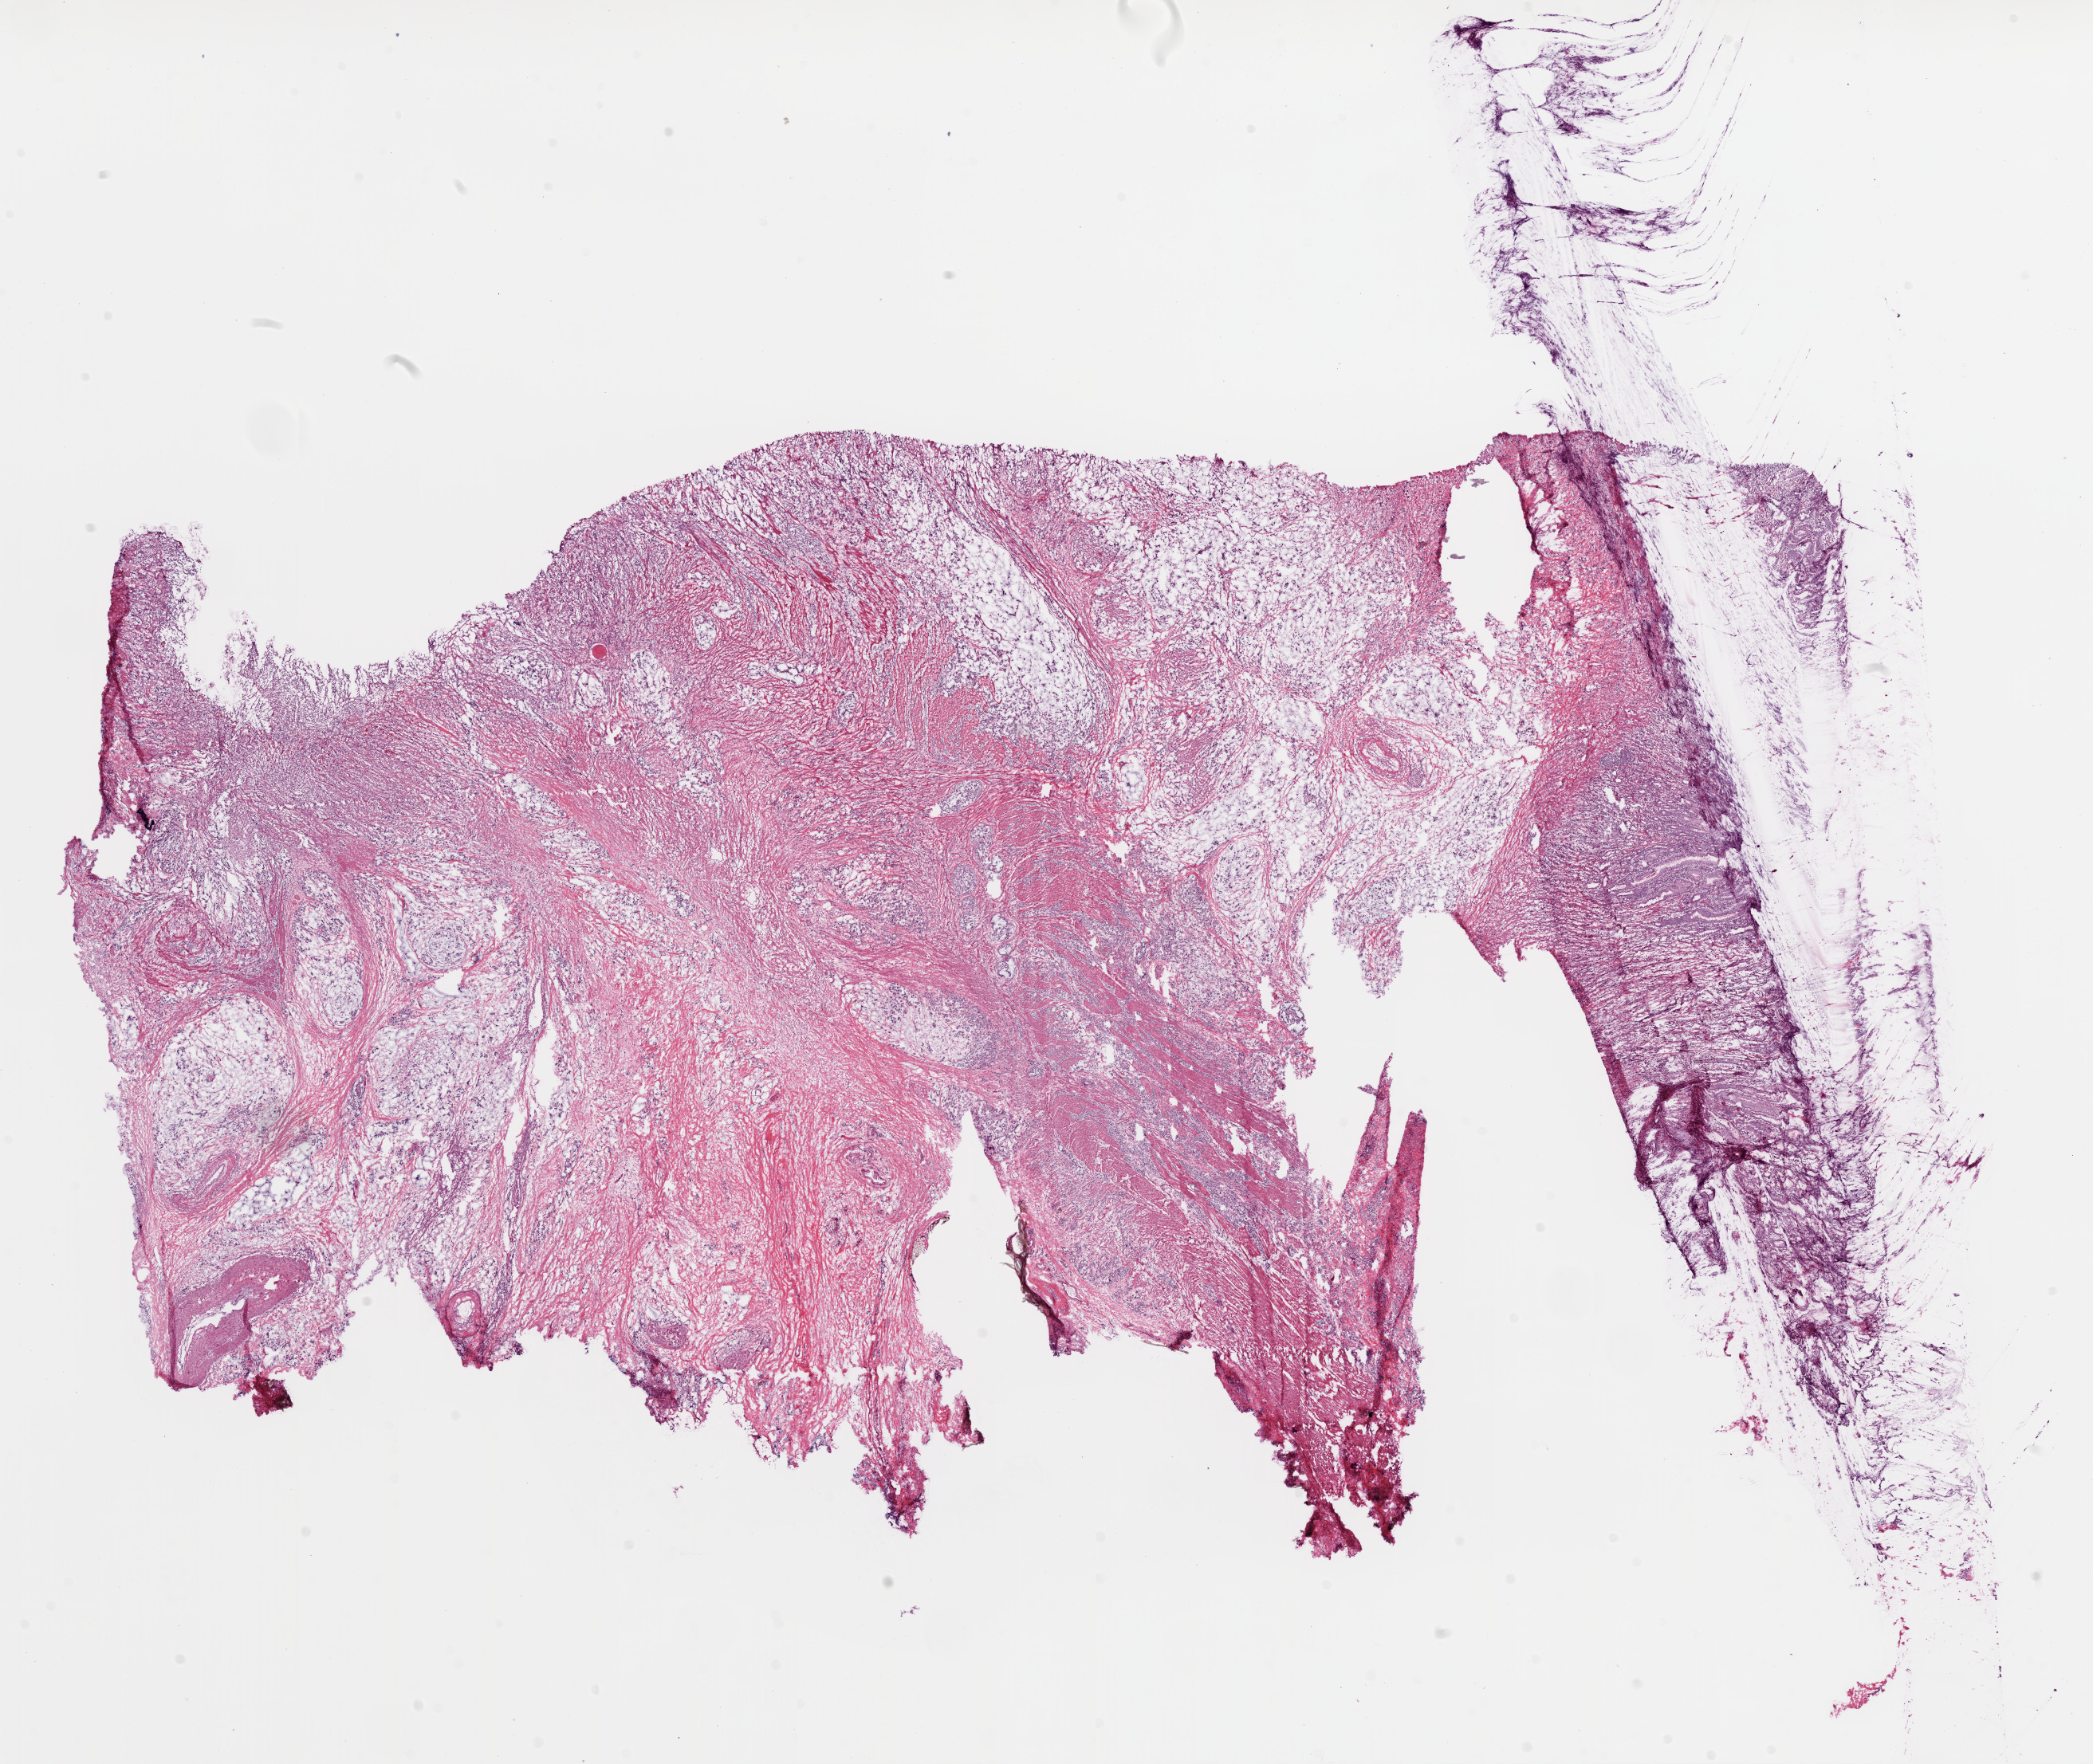
Whole-slide histology image, H&E-stained, shown as a low-resolution overview of the whole scanned area (about 21.1 x 17.8 mm, acquisition: 20x scan). Frozen section from the top of the tissue portion. Stomach, primary tumour sample. Male patient; age at initial diagnosis 43 years. Histologic grade: G3 (poorly differentiated). Slide review estimates, as recorded: tumour cells 52%, tumour nuclei 75%, normal cells 8%, stromal cells 40%, necrosis 0%.
• TNM: T2a N1 M0
• AJCC pathologic stage: II (6th edition)
• diagnosis: Adenocarcinoma, NOS
• lymph nodes positive (case pathology): 3 of 6 examined